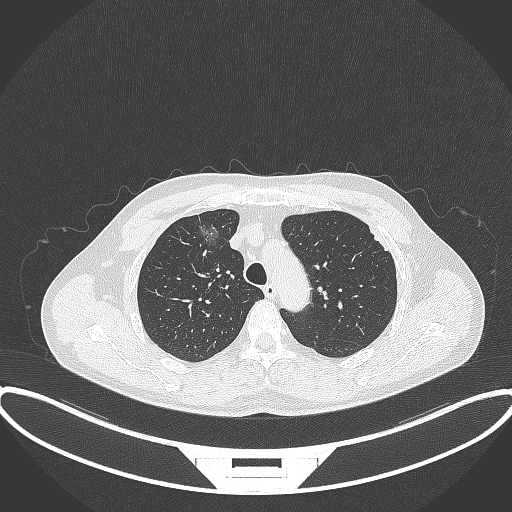
Chest CT, one axial slice. Position 277 of 395 along the scan axis. Reconstruction kernel B70f. 120 kVp. Lung window (W 1500 / L -600 HU). 512 × 512 image matrix. Male patient, age 60 years. Case-level facts recorded for this patient, not image findings: clinical TNM (as recorded): T1c N0 M0.
Outlined on this slice (rectangle marked by the reading radiologist):
- lung tumour (recorded histology: adenocarcinoma): bounding box <191,214,222,256> (left, top, right, bottom; pixels)